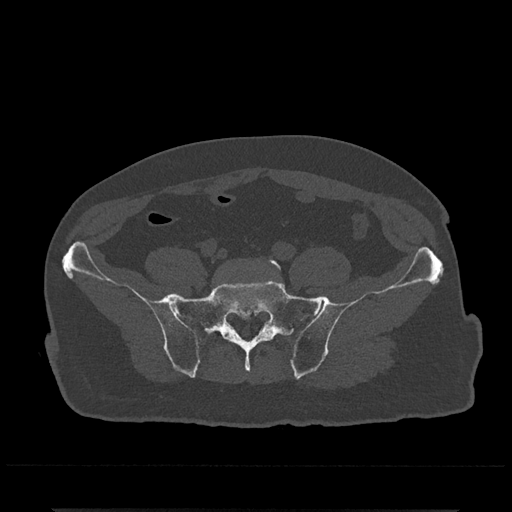
CT including the spine, one axial slice; position 31 of 797 along the scan axis; reconstruction kernel Br40s/3; bone window (W 1800 / L 400 HU); 512 × 512 image matrix. Male patient, age 67 years. From the clinical record (not read from this slice): primary cancer: prostate.
Structures marked on this image (semi-automatic segmentation, software-assisted and operator-edited):
- L5 vertebra: bounding box (x1, y1, x2, y2) in pixels: (269, 258, 281, 269)